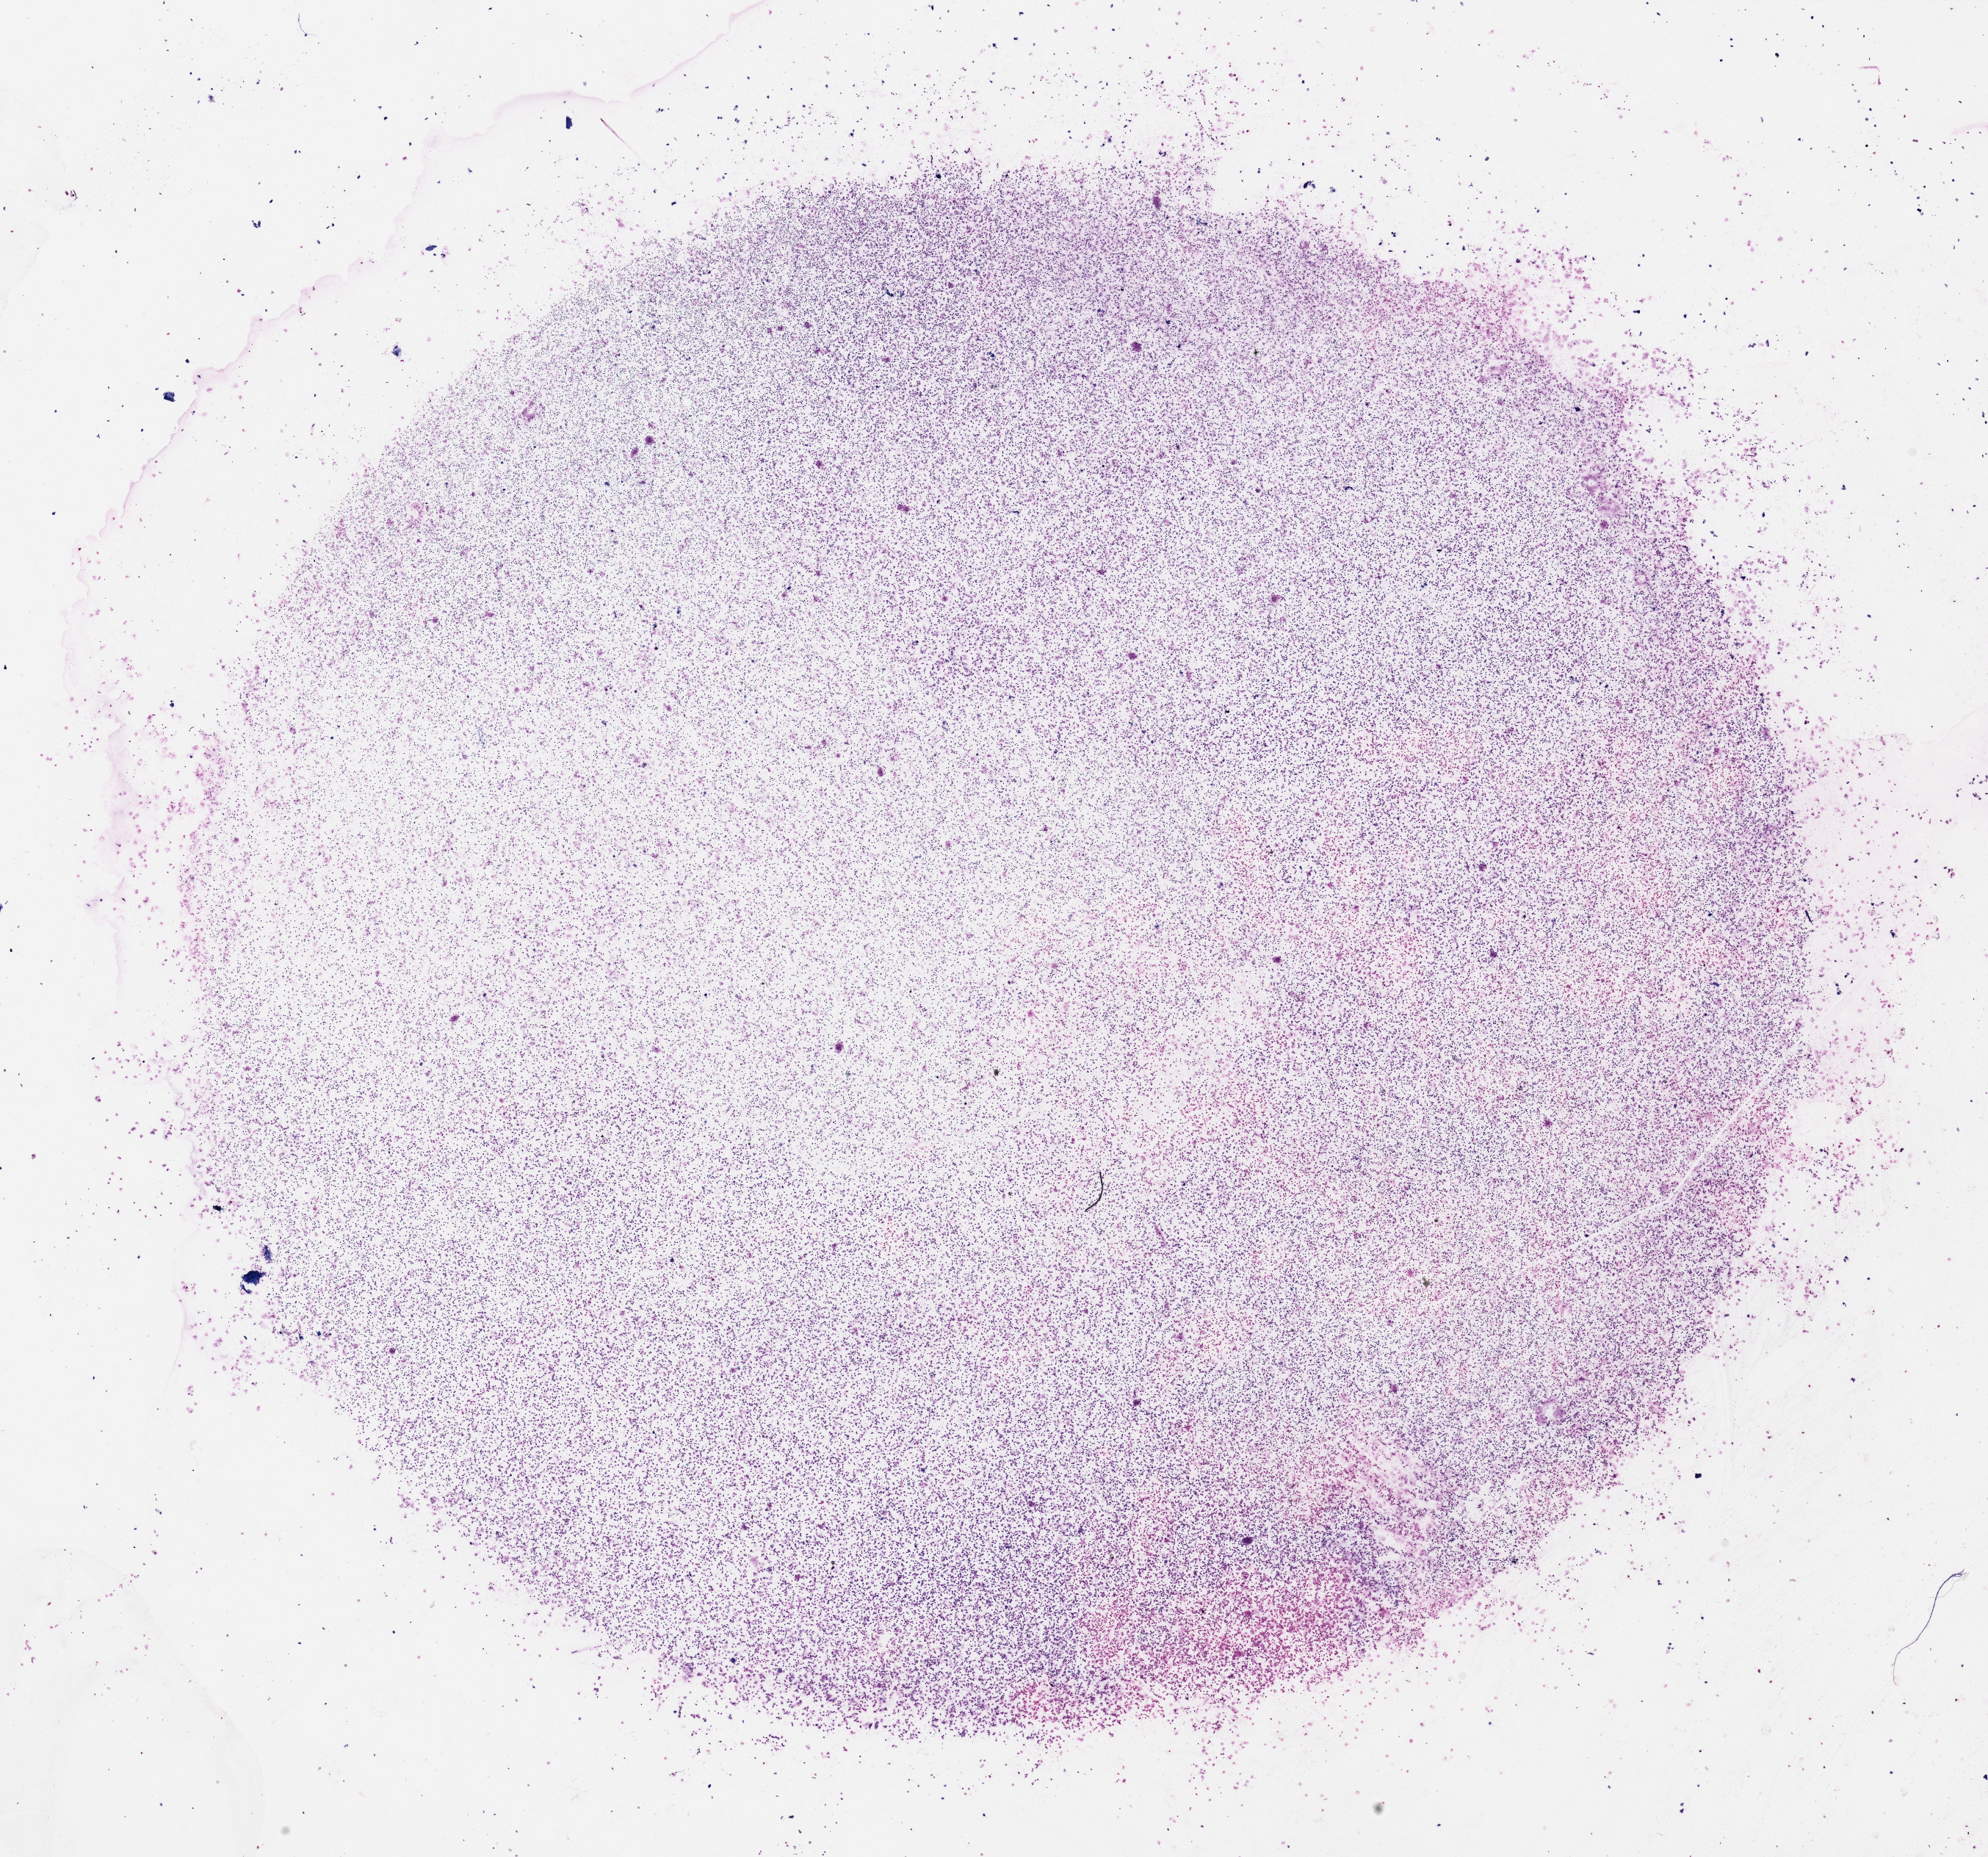
Whole-slide histology image, H&E, shown as a low-resolution overview of the whole scanned area (about 21.4 x 20.0 mm). Bone marrow (leukaemic) sample. Male, 70 y/o. Blasts: 90%.
Diagnosis: Acute Myeloid Leukemia. FAB classification: M1. WHO classification: AML without maturation.